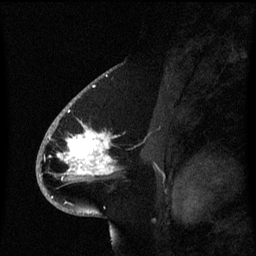
Breast MRI (dynamic contrast-enhanced), one sagittal slice. Slice 38 of 60 in the series (ordered by position). Dynamic contrast-enhanced series, image 2 of 3 at this slice position (ordered by acquisition). 1.5 T. TE 4.2 ms, TR 8.4 ms. 256 × 256 image matrix, field of view 200 × 200 mm. Patient: female, 53 years. Case-level facts recorded for this patient, not image findings: setting: breast cancer imaged before/during neoadjuvant chemotherapy; receptor status: HR-positive, HER2-negative.
Outlined on this slice (semi-automatic segmentation, software-assisted and operator-edited):
- analysis volume of interest (the breast-tissue region the enhancement analysis was run in; not a lesion): bounding box [x1, y1, x2, y2] px = [49, 108, 118, 201]
- tumour enhancement mask (voxels above the 70 % enhancement threshold inside the analysis volume of interest): [58, 126, 114, 175]